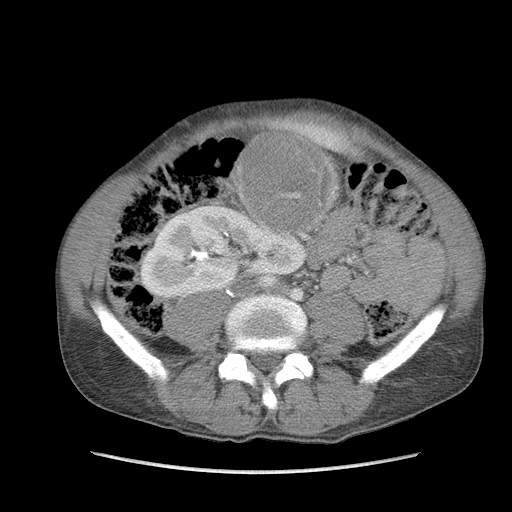
Contrast-enhanced abdominal CT, one axial slice; position 39 of 115 along the scan axis; soft-tissue window (W 400 / L 40 HU); 5 mm slice thickness; 512 × 512 image matrix, field of view 360 × 360 mm. Male patient. Case-level facts recorded for this patient, not image findings: diagnosis: adrenocortical carcinoma; tumour side: right adrenal; Ki-67 index: 13 %; stage (as recorded): 3.
Outlined on this slice (semi-automatically segmented with operator editing):
- mass: bounding box <244,135,328,228> (left, top, right, bottom; pixels)